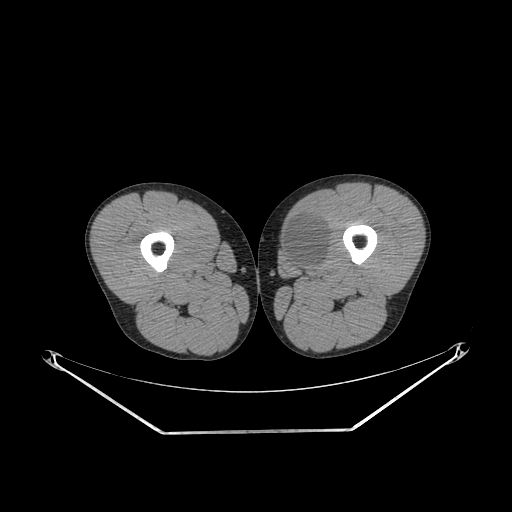
CT of an extremity soft-tissue mass (from a PET/CT study), one axial slice. Slice 250 of 311 in the series (ordered by position). Reconstruction kernel SOFT. Soft-tissue window (W 400 / L 40 HU). 3.75 mm slice thickness. 512 × 512 image matrix, field of view 500 × 500 mm. Male patient. From the clinical record (not read from this slice): histological type: mixoid liposarcoma; grade: low; site of the primary tumour: left thigh.
Outlined on this slice (expert contour drawn on MRI and transferred to this co-registered scan by the dataset authors):
- gross tumour volume (mass): bounding box (x1, y1, x2, y2) in pixels: (281, 215, 330, 270)